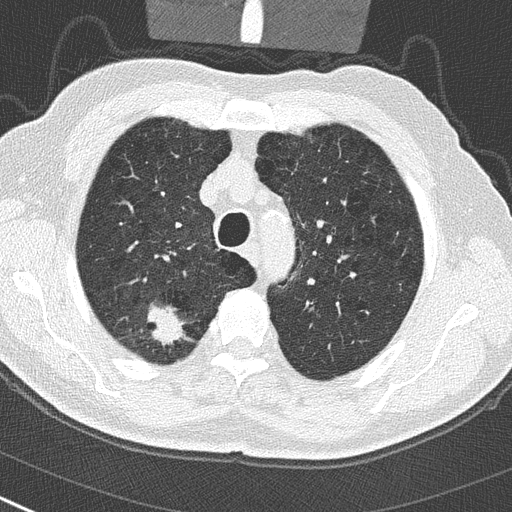
Axial slice from a low-dose chest CT screening exam. Baseline annual screen. Lung window (W 1500 / L -600 HU). Slice 65 of 290 in the series. 512 × 512 image matrix, field of view 300 × 300 mm. Male, age 65 years at enrolment.
Lesion marked by an expert reader, bounding box <132,300,195,357> (left, top, right, bottom; pixels). Reader record for this screening exam (exam-level; its link to the box is not recorded): non-calcified nodule or mass ≥4 mm, right upper lobe, 24 × 19 mm, spiculated (stellate) margins, soft tissue attenuation. Official screen result: positive, change unspecified: nodule(s) >= 4 mm or enlarging nodule(s), mass(es), or other non-specific abnormalities suspicious for lung cancer. Lung cancer was diagnosed 32 days after this screen: non-small cell carcinoma, right upper lobe, poorly differentiated (G3), stage IA (AJCC 6th edition), 29 mm at pathology.